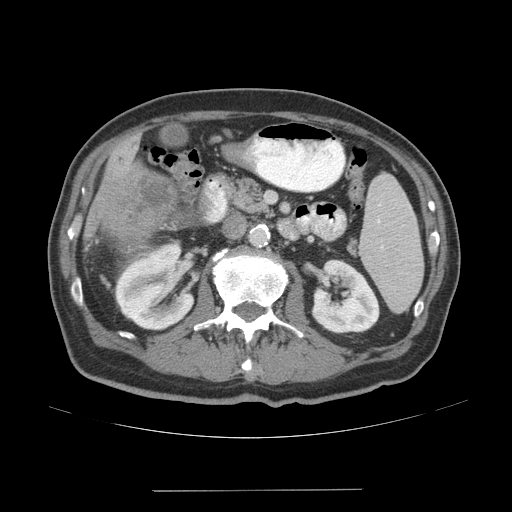
Contrast-enhanced abdominal CT (liver protocol), one axial slice. Position 11 of 77 along the scan axis. 140 kVp. Soft-tissue window (W 400 / L 40 HU). 2.5 mm slice thickness. 512 × 512 image matrix, field of view 400 × 400 mm. From the clinical record (not read from this slice): diagnosis: hepatocellular carcinoma (patient treated with transarterial chemoembolisation; whether this scan precedes or follows treatment is not stated here); TNM stage (as recorded): Stage-IVA; Child-Pugh class: A; tumour differentiation: well differentiated; tumour nodularity: uninodular.
Annotated regions visible in this slice (semi-automatically segmented with operator editing):
- liver parenchyma outside the tumour (the mass and vessels are separate outlines, so this box may not span the whole liver): bounding box <84,138,175,254> (left, top, right, bottom; pixels)
- mass: <108,170,181,246>